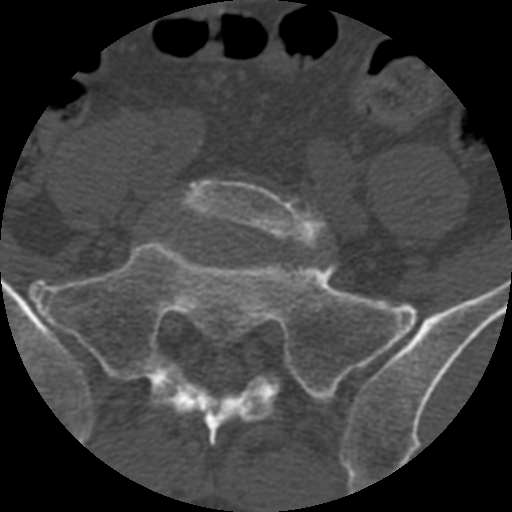
CT including the spine, one axial slice; slice 237 of 399 in the series (ordered by position); reconstruction kernel STANDARD; bone window (W 1800 / L 400 HU); 1.25 mm slice thickness; 512 × 512 image matrix, field of view 160 × 160 mm. Patient age 71 years. From the clinical record (not read from this slice): primary cancer: prostate.
Outlined on this slice (semi-automatically segmented with operator editing):
- L5 vertebra: bounding box (x1, y1, x2, y2) in pixels: (176, 179, 328, 249)